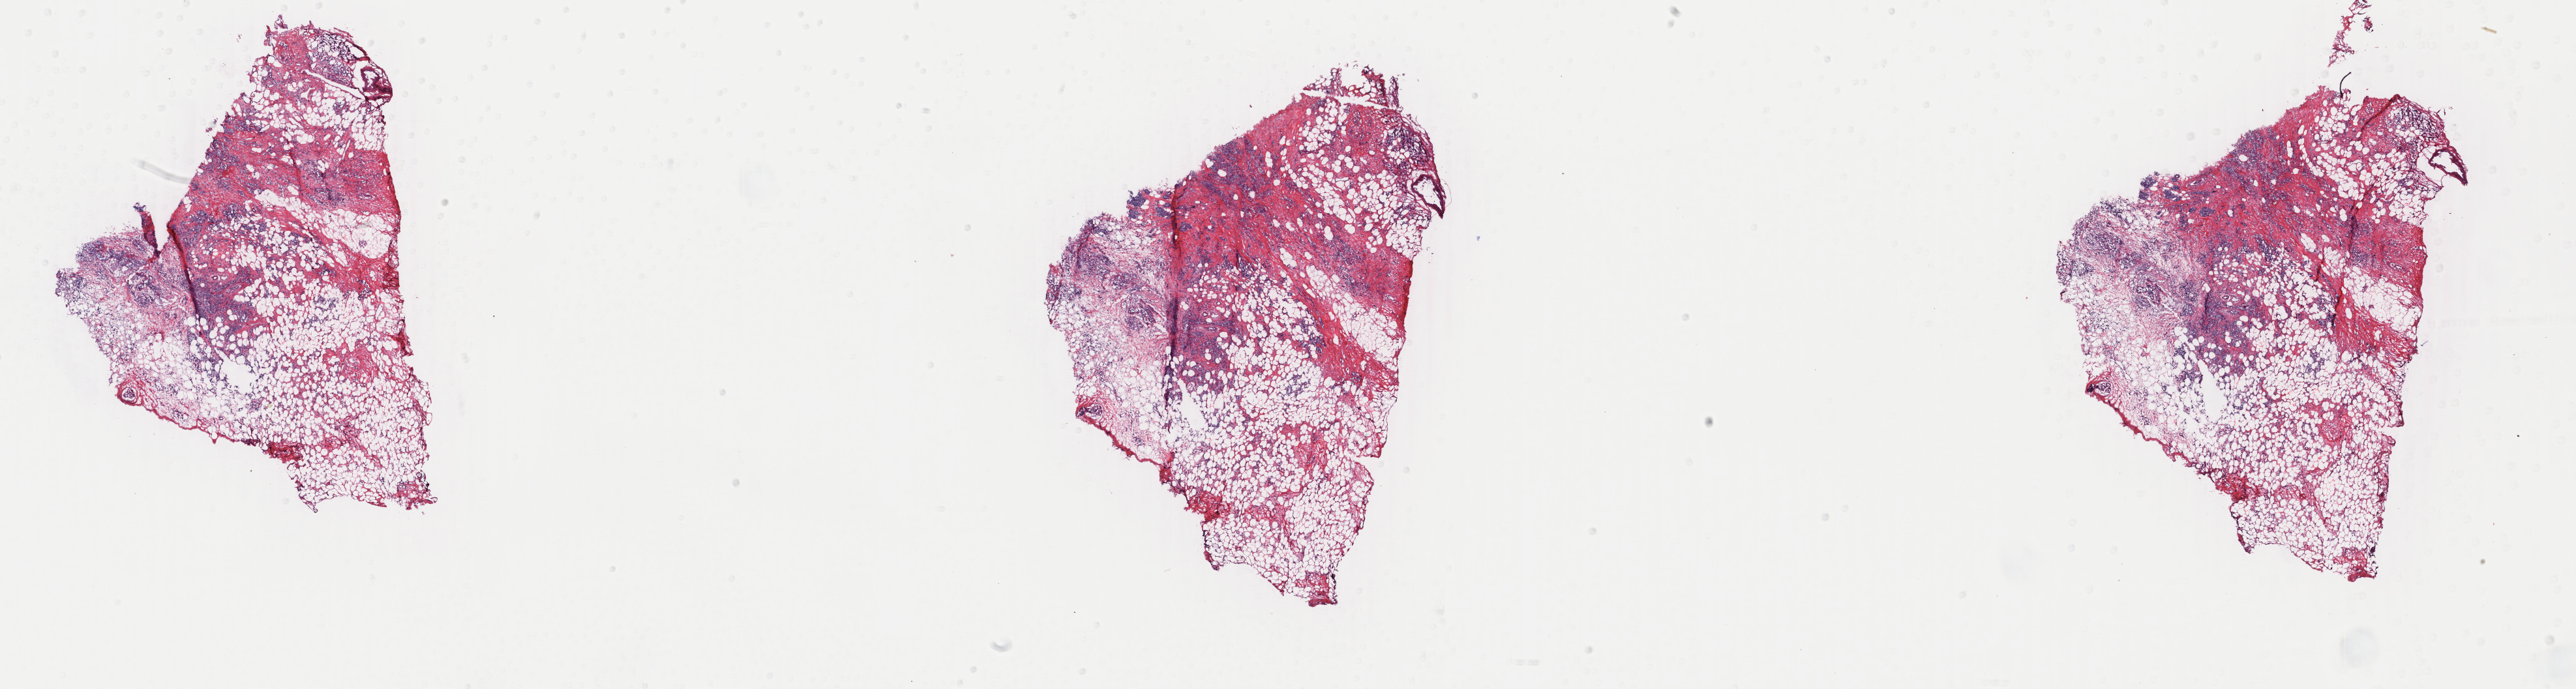
Whole-slide histology image, H&E-stained — whole scanned area (about 31.4 x 8.4 mm, slide scanned at 40x) shown as a low-resolution overview, frozen section from the top of the tissue portion, primary tumour sample from the breast. Patient sex: female. Pathologist review of this section (percent, as recorded): tumour cells 40%, tumour nuclei 50%, normal cells 0%, stromal cells 60%, necrosis 0%. Inflammatory infiltration, as recorded: lymphocyte infiltration 0%, monocyte infiltration 0%, neutrophil infiltration 0%.
- AJCC pathologic stage: IIB
- laterality: right
- diagnosis: Lobular carcinoma, NOS
- lymph nodes positive (case pathology): 0 of 11 examined